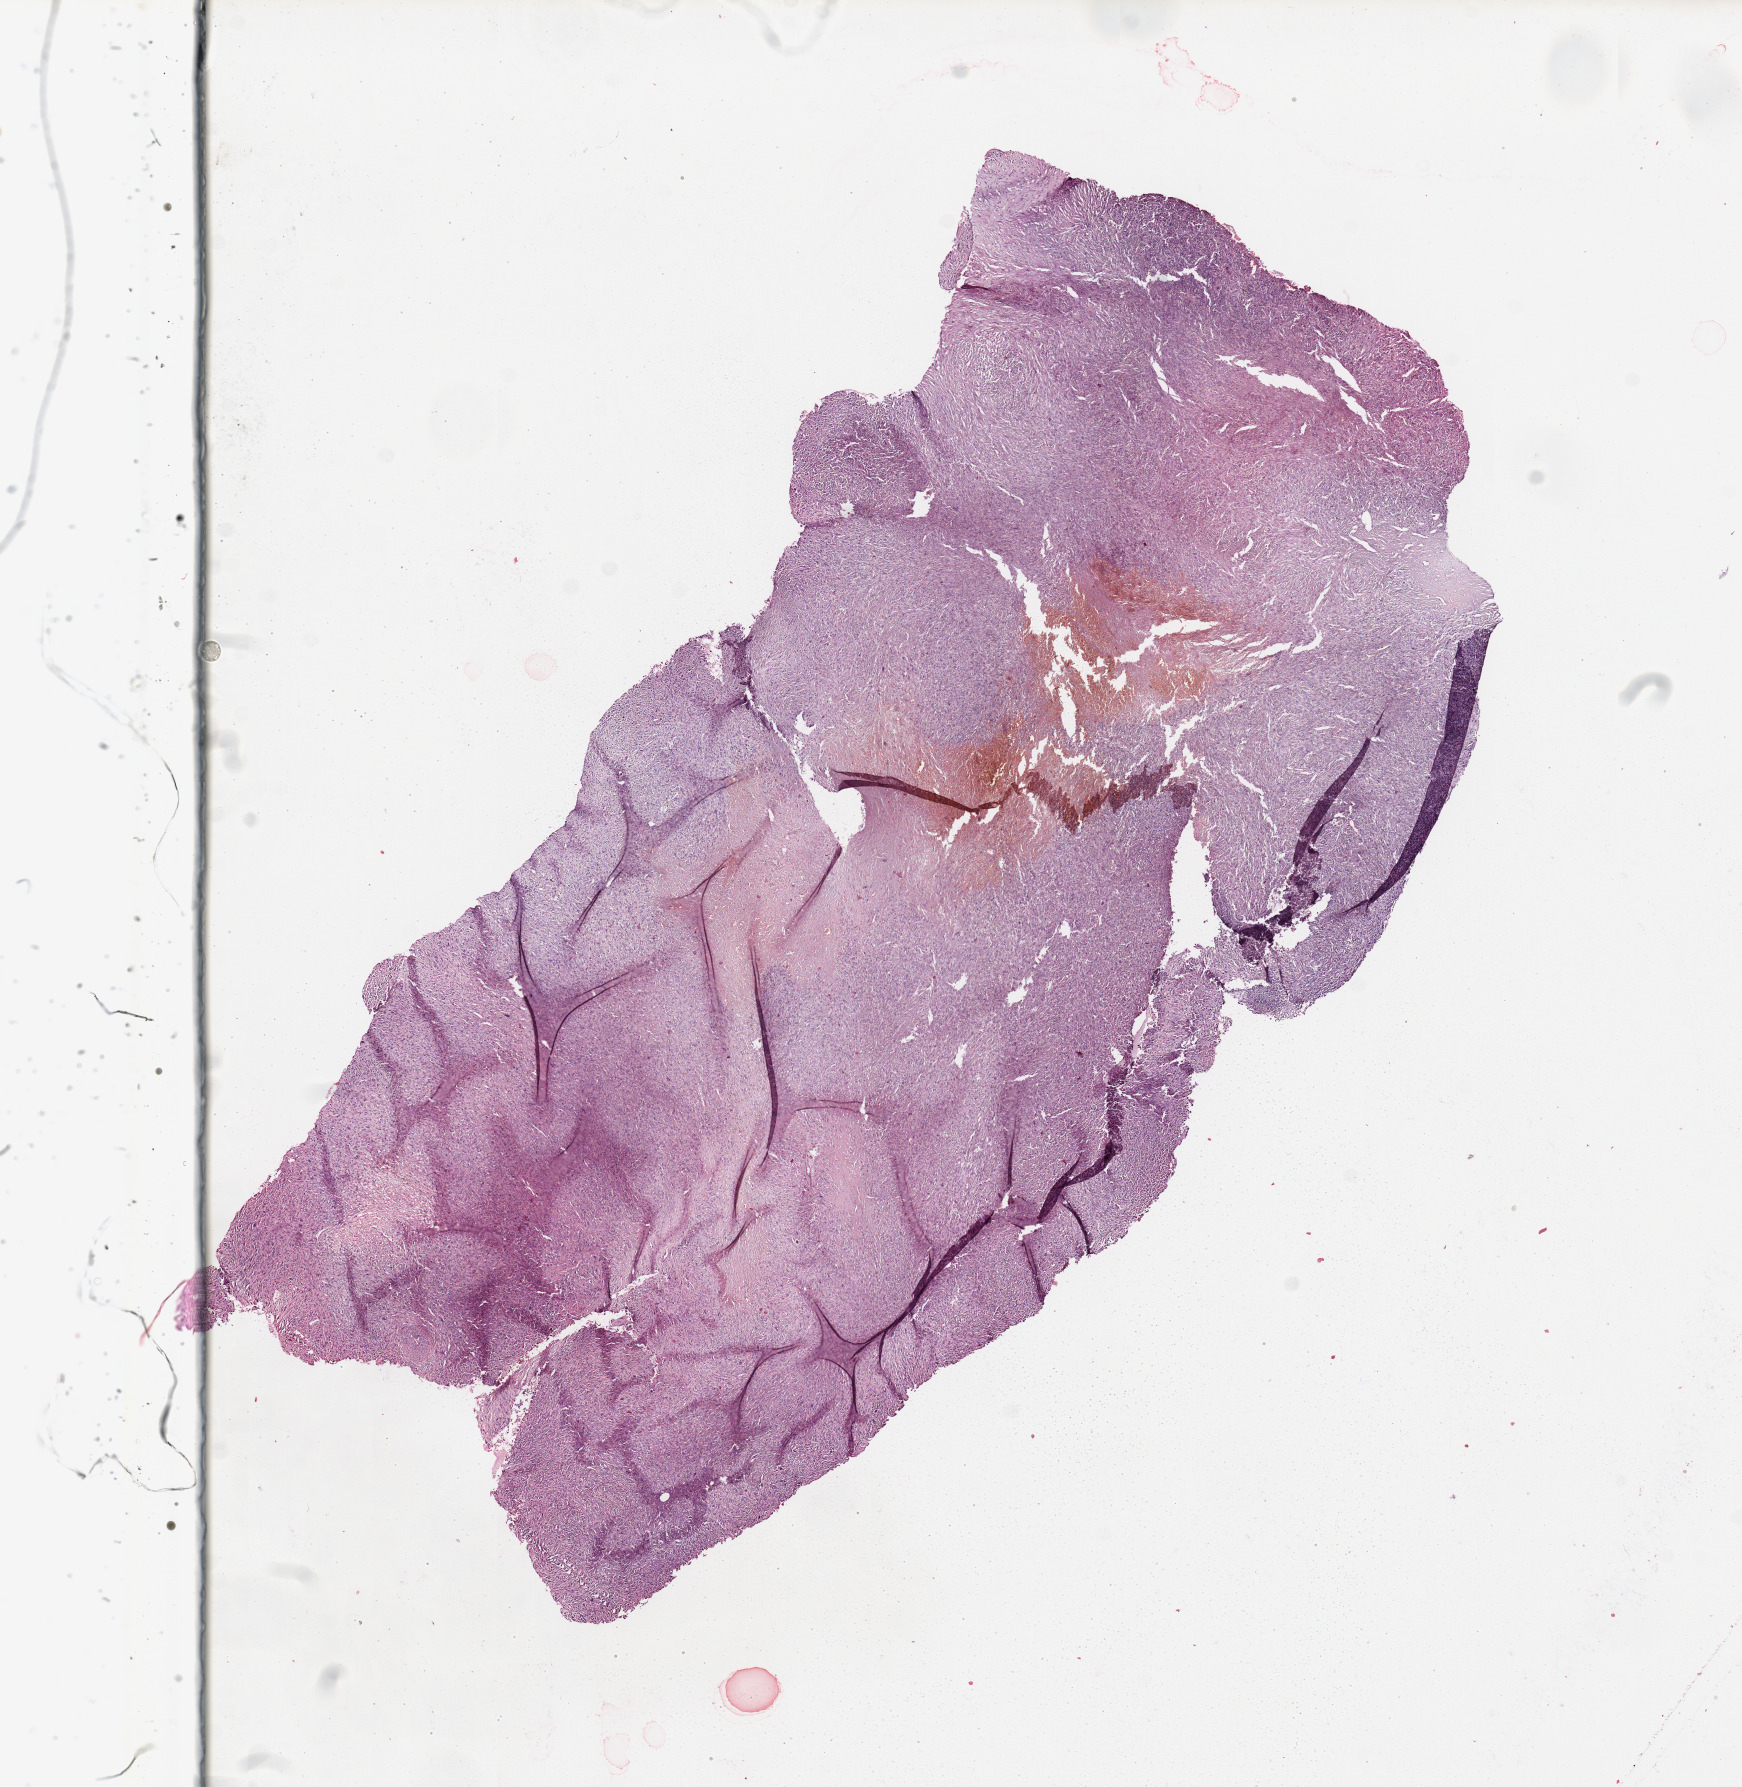
H&E-stained whole-slide image, shown as a low-resolution overview of the whole scanned area (about 13.8 x 14.1 mm). Tumour tissue sample. Patient: male, age 53 years.
Patient diagnosis (cohort enrolment): sarcoma (site not recorded at cohort level).